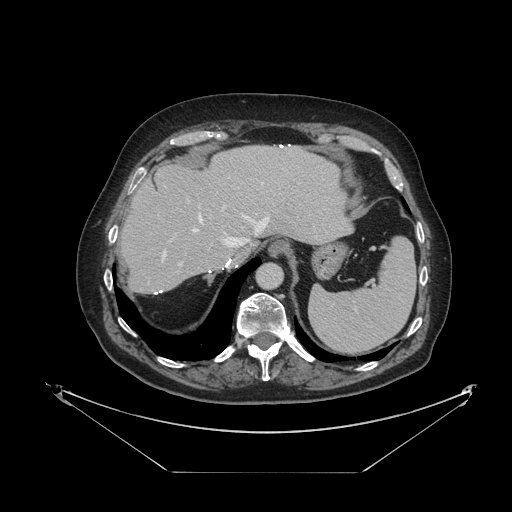
Contrast-enhanced abdominal CT, one axial slice; slice 88 of 121 in the series (ordered by position); intravenous contrast given; soft-tissue window (W 400 / L 40 HU); 2.5 mm slice thickness; 512 × 512 image matrix. Male patient, age 68 years. Case-level facts recorded for this patient, not image findings: diagnosis: colorectal cancer liver metastases, imaged before liver resection; multiple liver metastases: no; largest metastasis: 4 cm; disease in both lobes: no.
Annotated regions visible in this slice (outlined manually by an expert reader):
- hepatic veins: box from (x=163, y=147) to (x=282, y=258) px
- liver: (x=121, y=146)–(x=351, y=294)
- planned liver remnant (the part of the liver to remain after resection): (x=121, y=146)–(x=351, y=293)
- portal vein (with intrahepatic branches): (x=178, y=192)–(x=226, y=266)